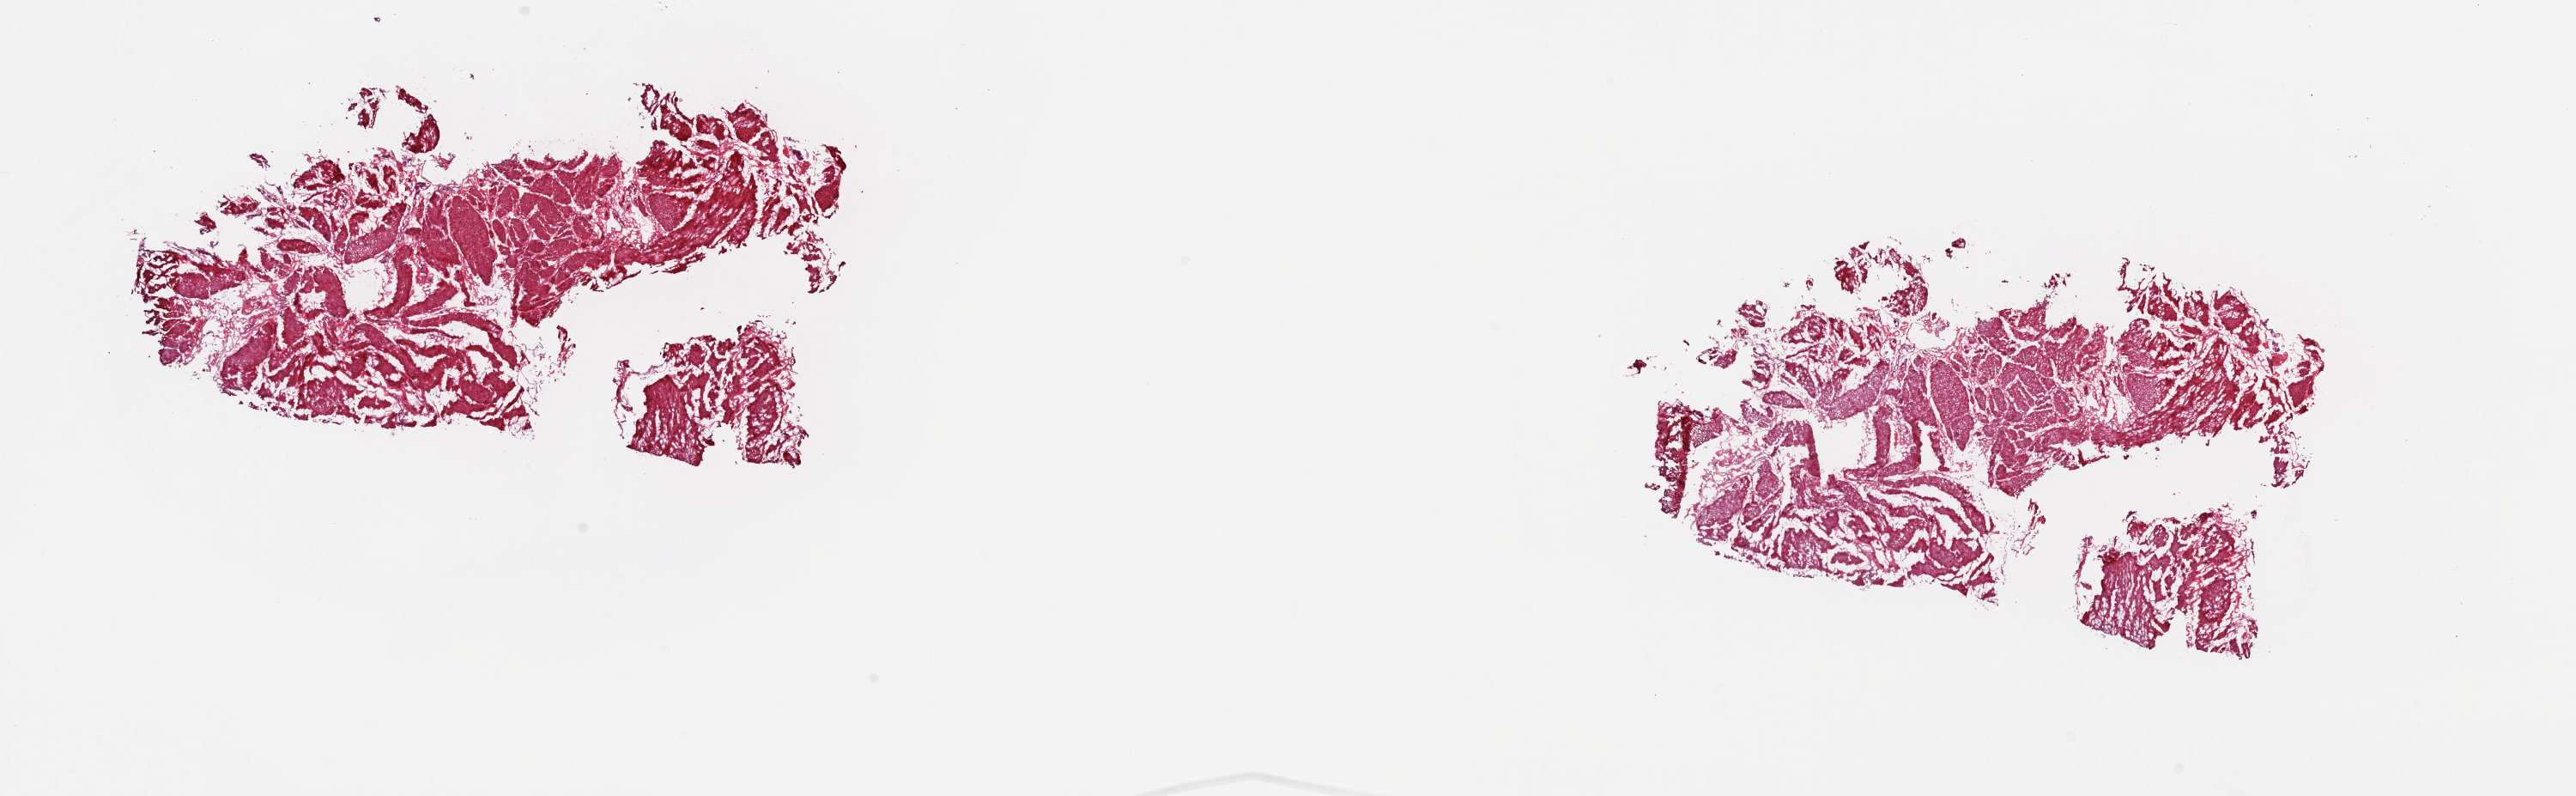
Hematoxylin and eosin (H&E) stained whole-slide image, low-resolution overview of the scanned area, about 23.8 x 7.4 mm, frozen section from the top of the tissue portion, sample: solid tissue normal (non-tumour tissue), bladder. Patient: male, age at initial diagnosis 62 years. Composition of this section per pathologist review: tumour cells 0%, tumour nuclei 0%, normal cells 100%, stromal cells 0%, necrosis 0%. Inflammatory infiltration, as recorded: lymphocyte infiltration 0%, monocyte infiltration 0%, neutrophil infiltration 0%.
This section: solid tissue normal (non-tumour) sample from the same patient. Patient diagnosis: Transitional cell carcinoma.